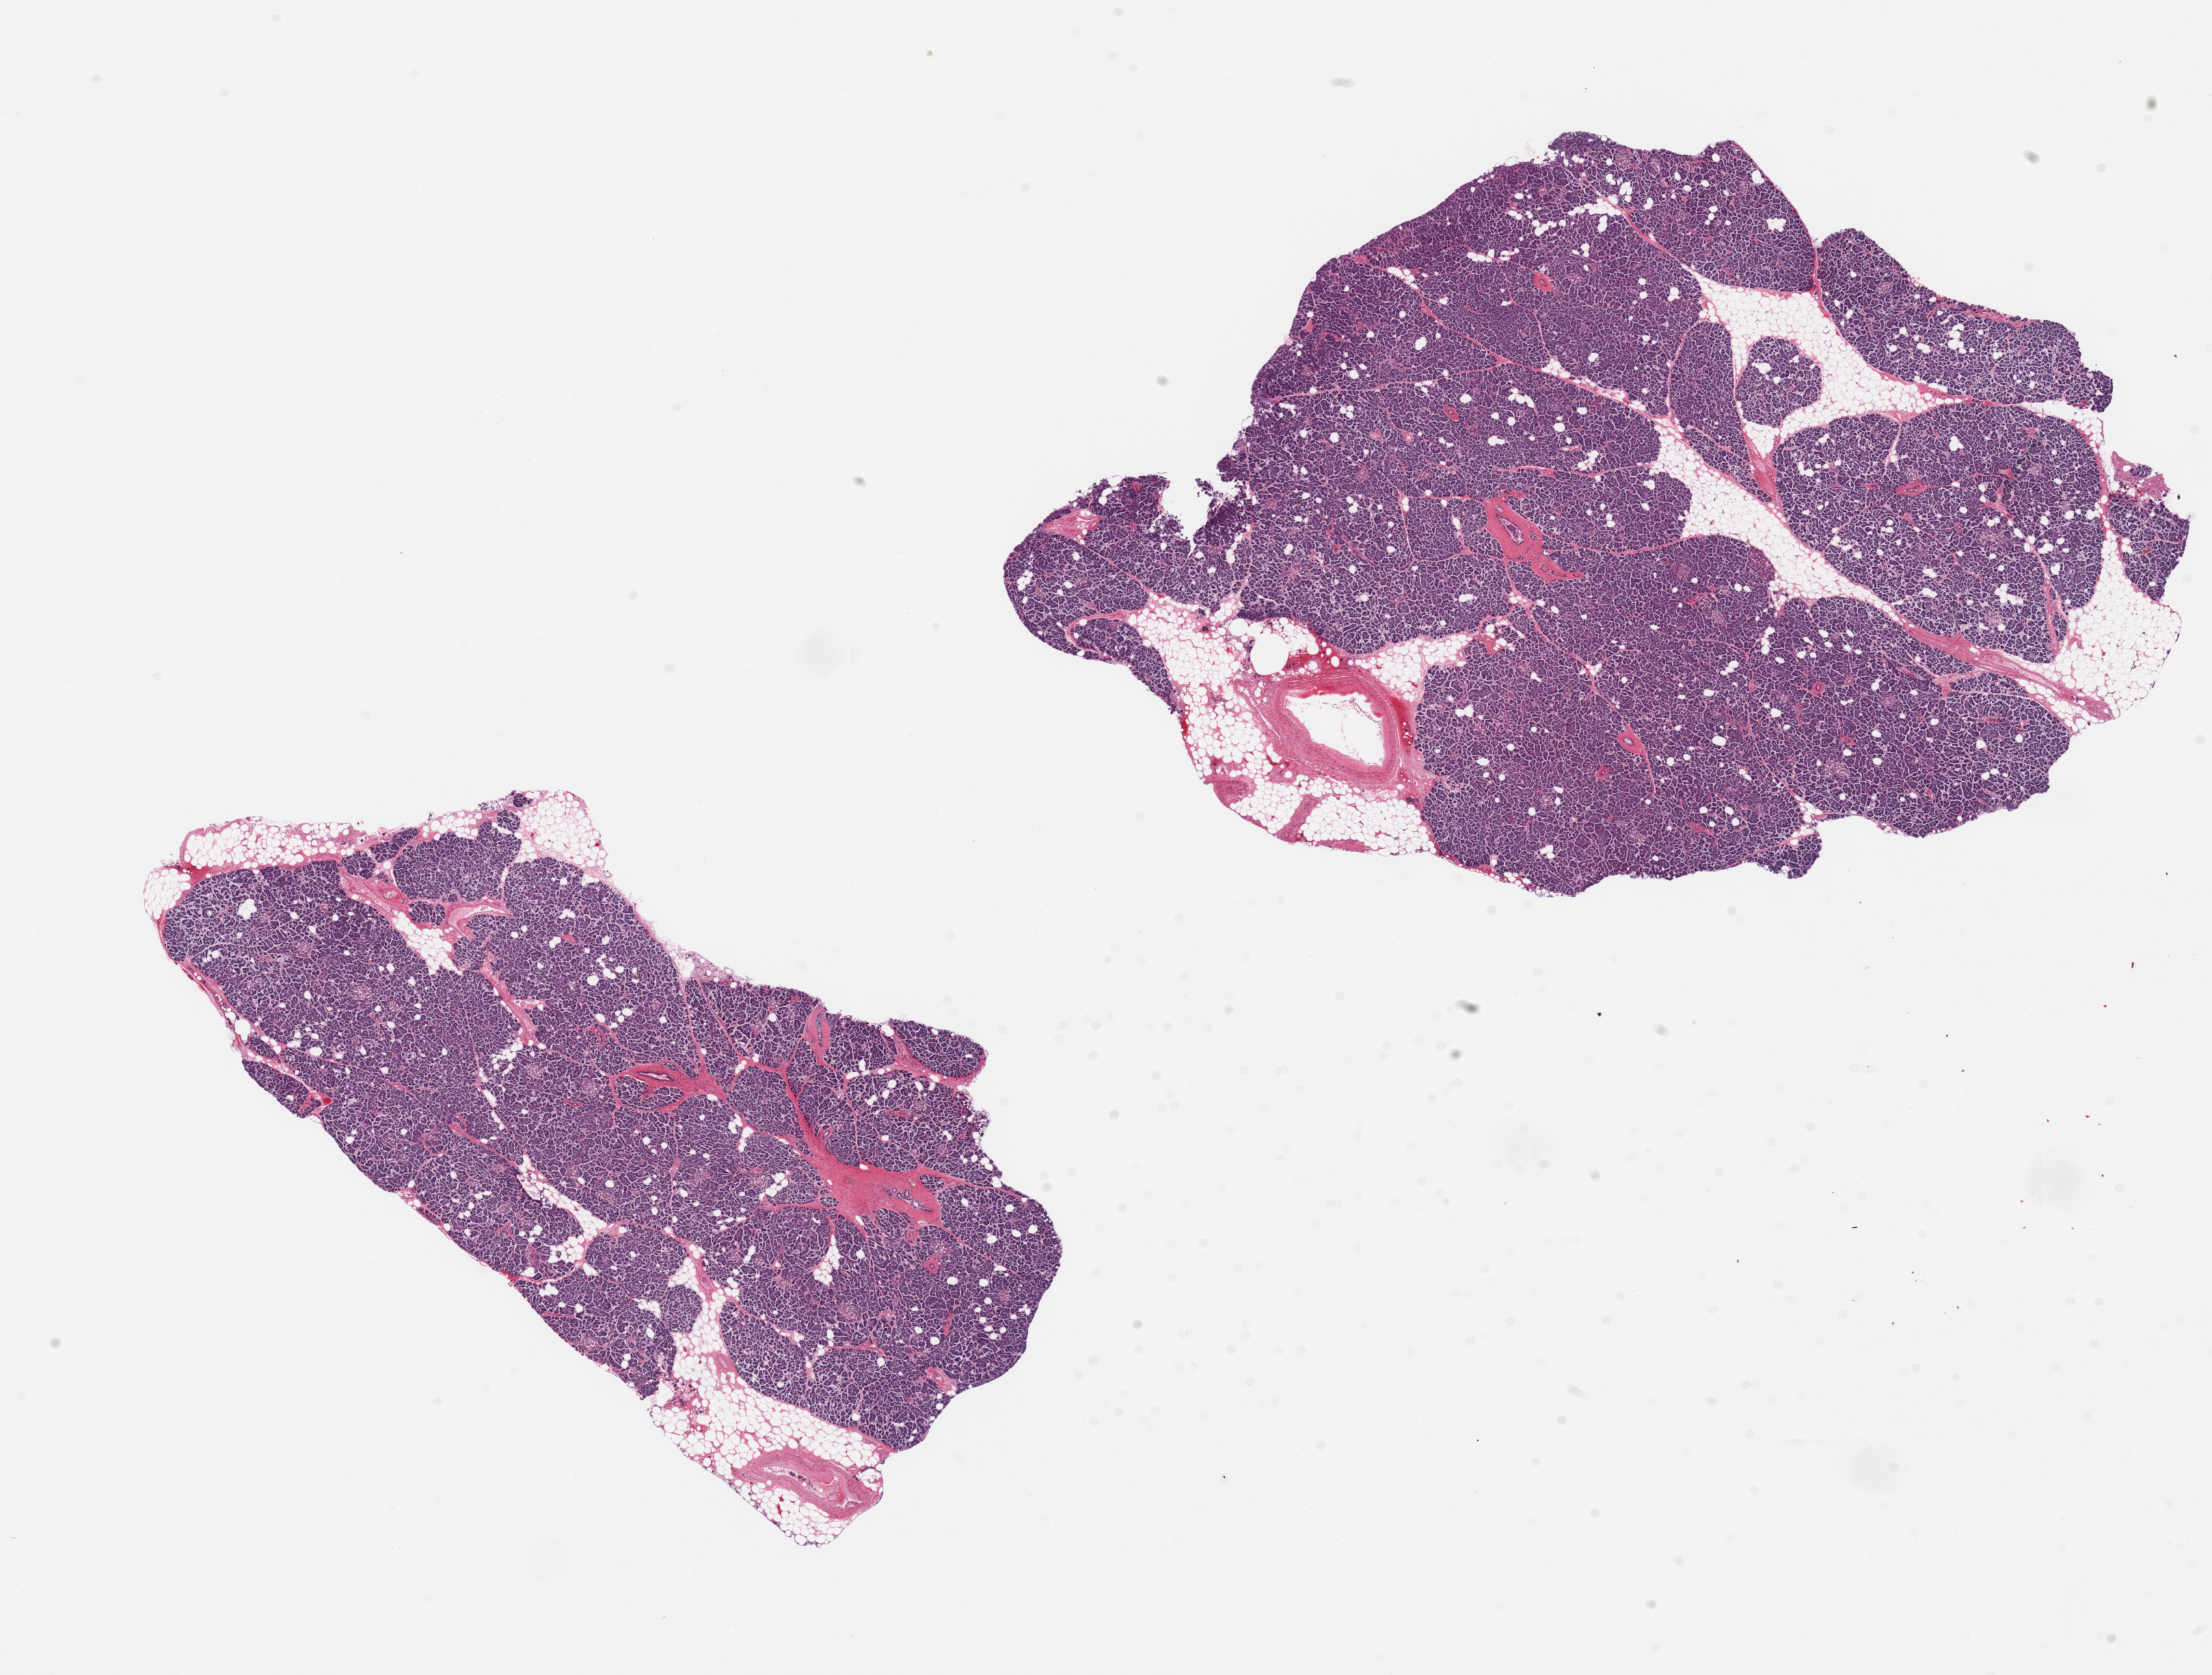
Digitized haematoxylin and eosin-stained section, shown as a low-resolution overview of the whole scanned area (about 25.6 x 19.4 mm); PAXgene-fixed, paraffin-embedded tissue; sampled site (target tissue): pancreas; donor tissue sample. Donor: male.
* reviewer comment on this tissue sample: 2 pieces; 20% internal fat